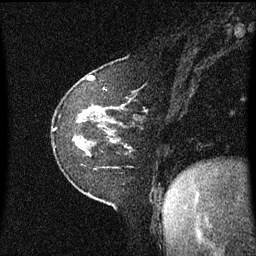
Breast MRI (dynamic contrast-enhanced), one sagittal slice. Slice 18 of 60 in the series (ordered by position). Dynamic contrast-enhanced series, image 2 of 3 at this slice position (ordered by acquisition). 1.5 T. TE 4.2 ms, TR 8.4 ms. 2 mm slice thickness. 256 × 256 image matrix. Female patient, age 60 years. Case-level facts recorded for this patient, not image findings: setting: breast cancer imaged before/during neoadjuvant chemotherapy; receptor status: triple-negative.
Annotated regions visible in this slice (semi-automatic segmentation, software-assisted and operator-edited):
- analysis volume of interest (the breast-tissue region the enhancement analysis was run in; not a lesion): bounding box (x1, y1, x2, y2) in pixels: (53, 105, 125, 168)
- tumour enhancement mask (voxels above the 70 % enhancement threshold inside the analysis volume of interest): (84, 107, 100, 114)